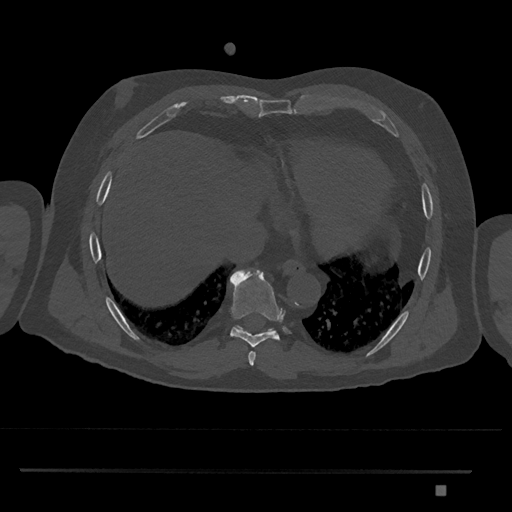
CT including the spine, one axial slice. Position 1102 of 1134 along the scan axis. 120 kVp. Bone window (W 1800 / L 400 HU). 512 × 512 image matrix. Male patient, age 65 years. From the clinical record (not read from this slice): primary cancer: prostate.
Structures marked on this image (semi-automatic segmentation, software-assisted and operator-edited):
- T8 vertebra: box from (x=230, y=269) to (x=283, y=347) px
- T9 vertebra: (x=235, y=325)–(x=274, y=332)